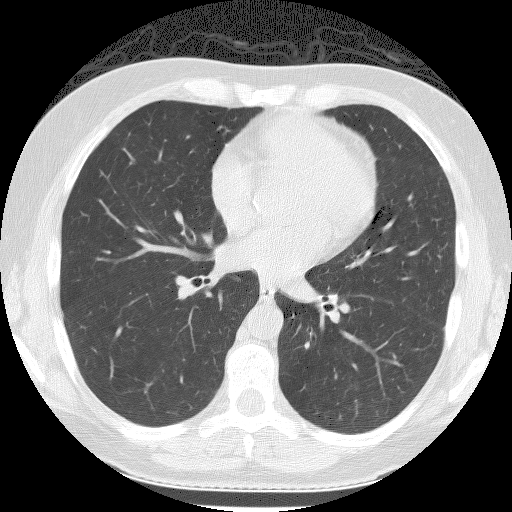
Axial slice from a low-dose chest CT screening exam, first (baseline) screen, lung window (W 1500 / L -600 HU), 120 kVp, 512 × 512 image matrix. Female, age 60 years at enrolment.
Expert-annotated lung lesion, bounding box (x1, y1, x2, y2) in pixels: (316, 363, 350, 393). No non-calcified nodule or mass ≥4 mm was recorded by the screening reader at this exam. Later outcome: lung cancer diagnosed 385 days after this screen — small cell carcinoma, NOS, left lower lobe, stage IIA (AJCC 6th edition), 12 mm at pathology.